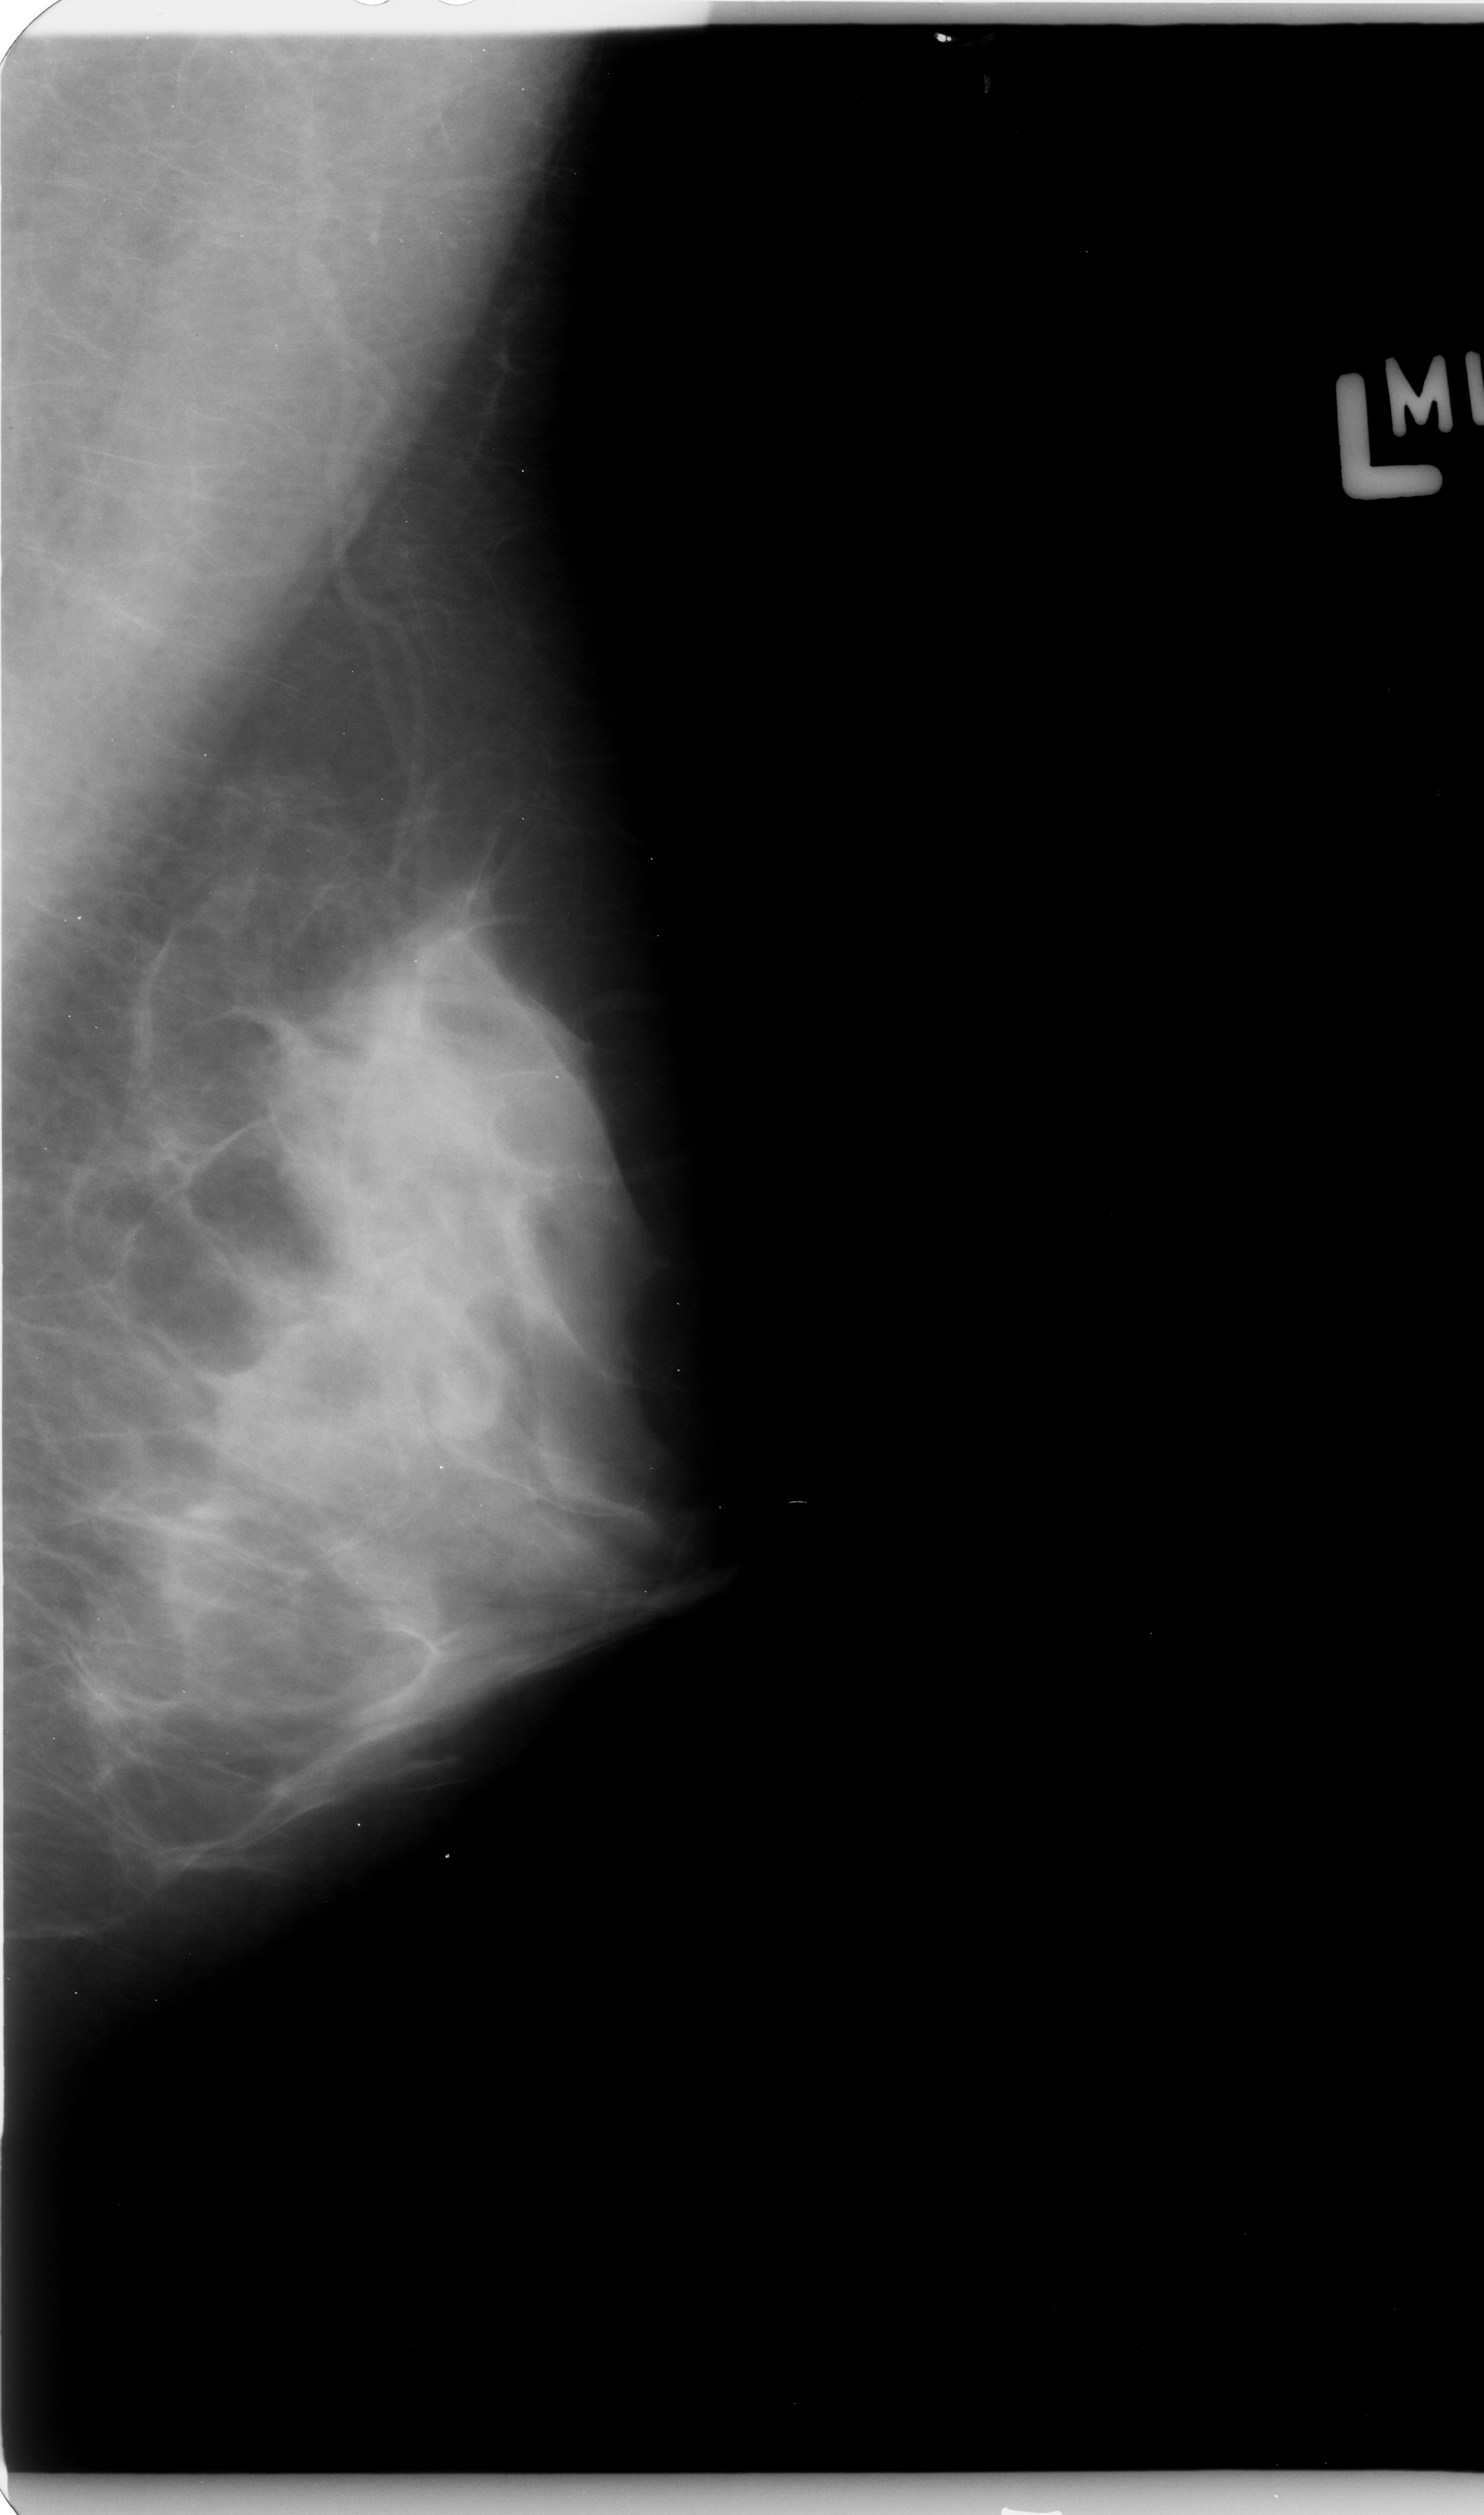
Scanned film-screen mammogram. Left breast. MLO view. BI-RADS breast density category 4 (scale 1–4). 1484 × 2515 image matrix.
Expert-marked regions of interest on this image (one box per marked abnormality):
- mass, shape round, margins circumscribed; BI-RADS assessment category 3; pathology result (as recorded, not read from the image): benign: bounding box [x1, y1, x2, y2] px = [433, 1364, 515, 1446]